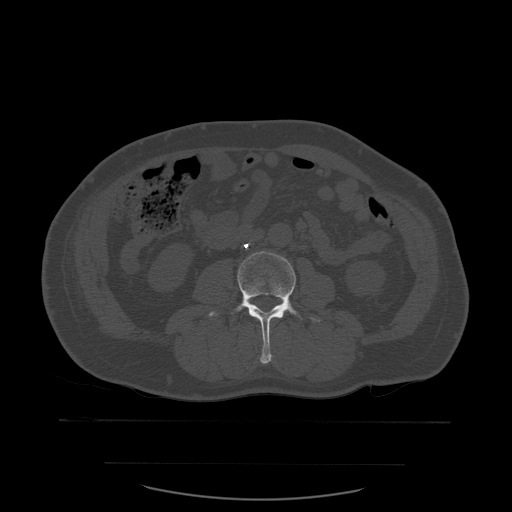
CT including the spine, one axial slice; slice 191 of 590 in the series (ordered by position); bone window (W 1800 / L 400 HU); 1.25 mm slice thickness; 512 × 512 image matrix. Patient age 71 years. From the clinical record (not read from this slice): primary cancer: lung; vertebrae with lytic lesions (as recorded): T1, T2, L5, S1.
Annotated regions visible in this slice (semi-automatic segmentation, software-assisted and operator-edited):
- L3 vertebra: bounding box <209,251,322,364> (left, top, right, bottom; pixels)